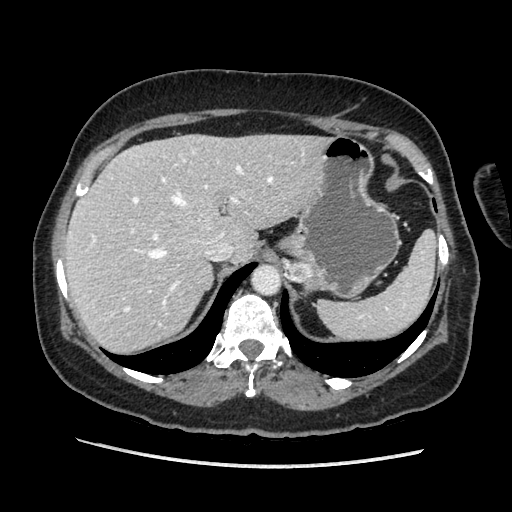
Contrast-enhanced abdominal CT, one axial slice; slice 147 of 203 in the series (ordered by position); soft-tissue window (W 400 / L 40 HU); 1.25 mm slice thickness; 512 × 512 image matrix. Female patient. Case-level facts recorded for this patient, not image findings: diagnosis: adrenocortical carcinoma; tumour side: left adrenal; tumour size at pathology: 6.5 cm; Ki-67 index: 22 %; stage (as recorded): 2.
Structures marked on this image (semi-automatic segmentation, software-assisted and operator-edited):
- mass: bounding box (x1, y1, x2, y2) in pixels: (289, 262, 313, 283)